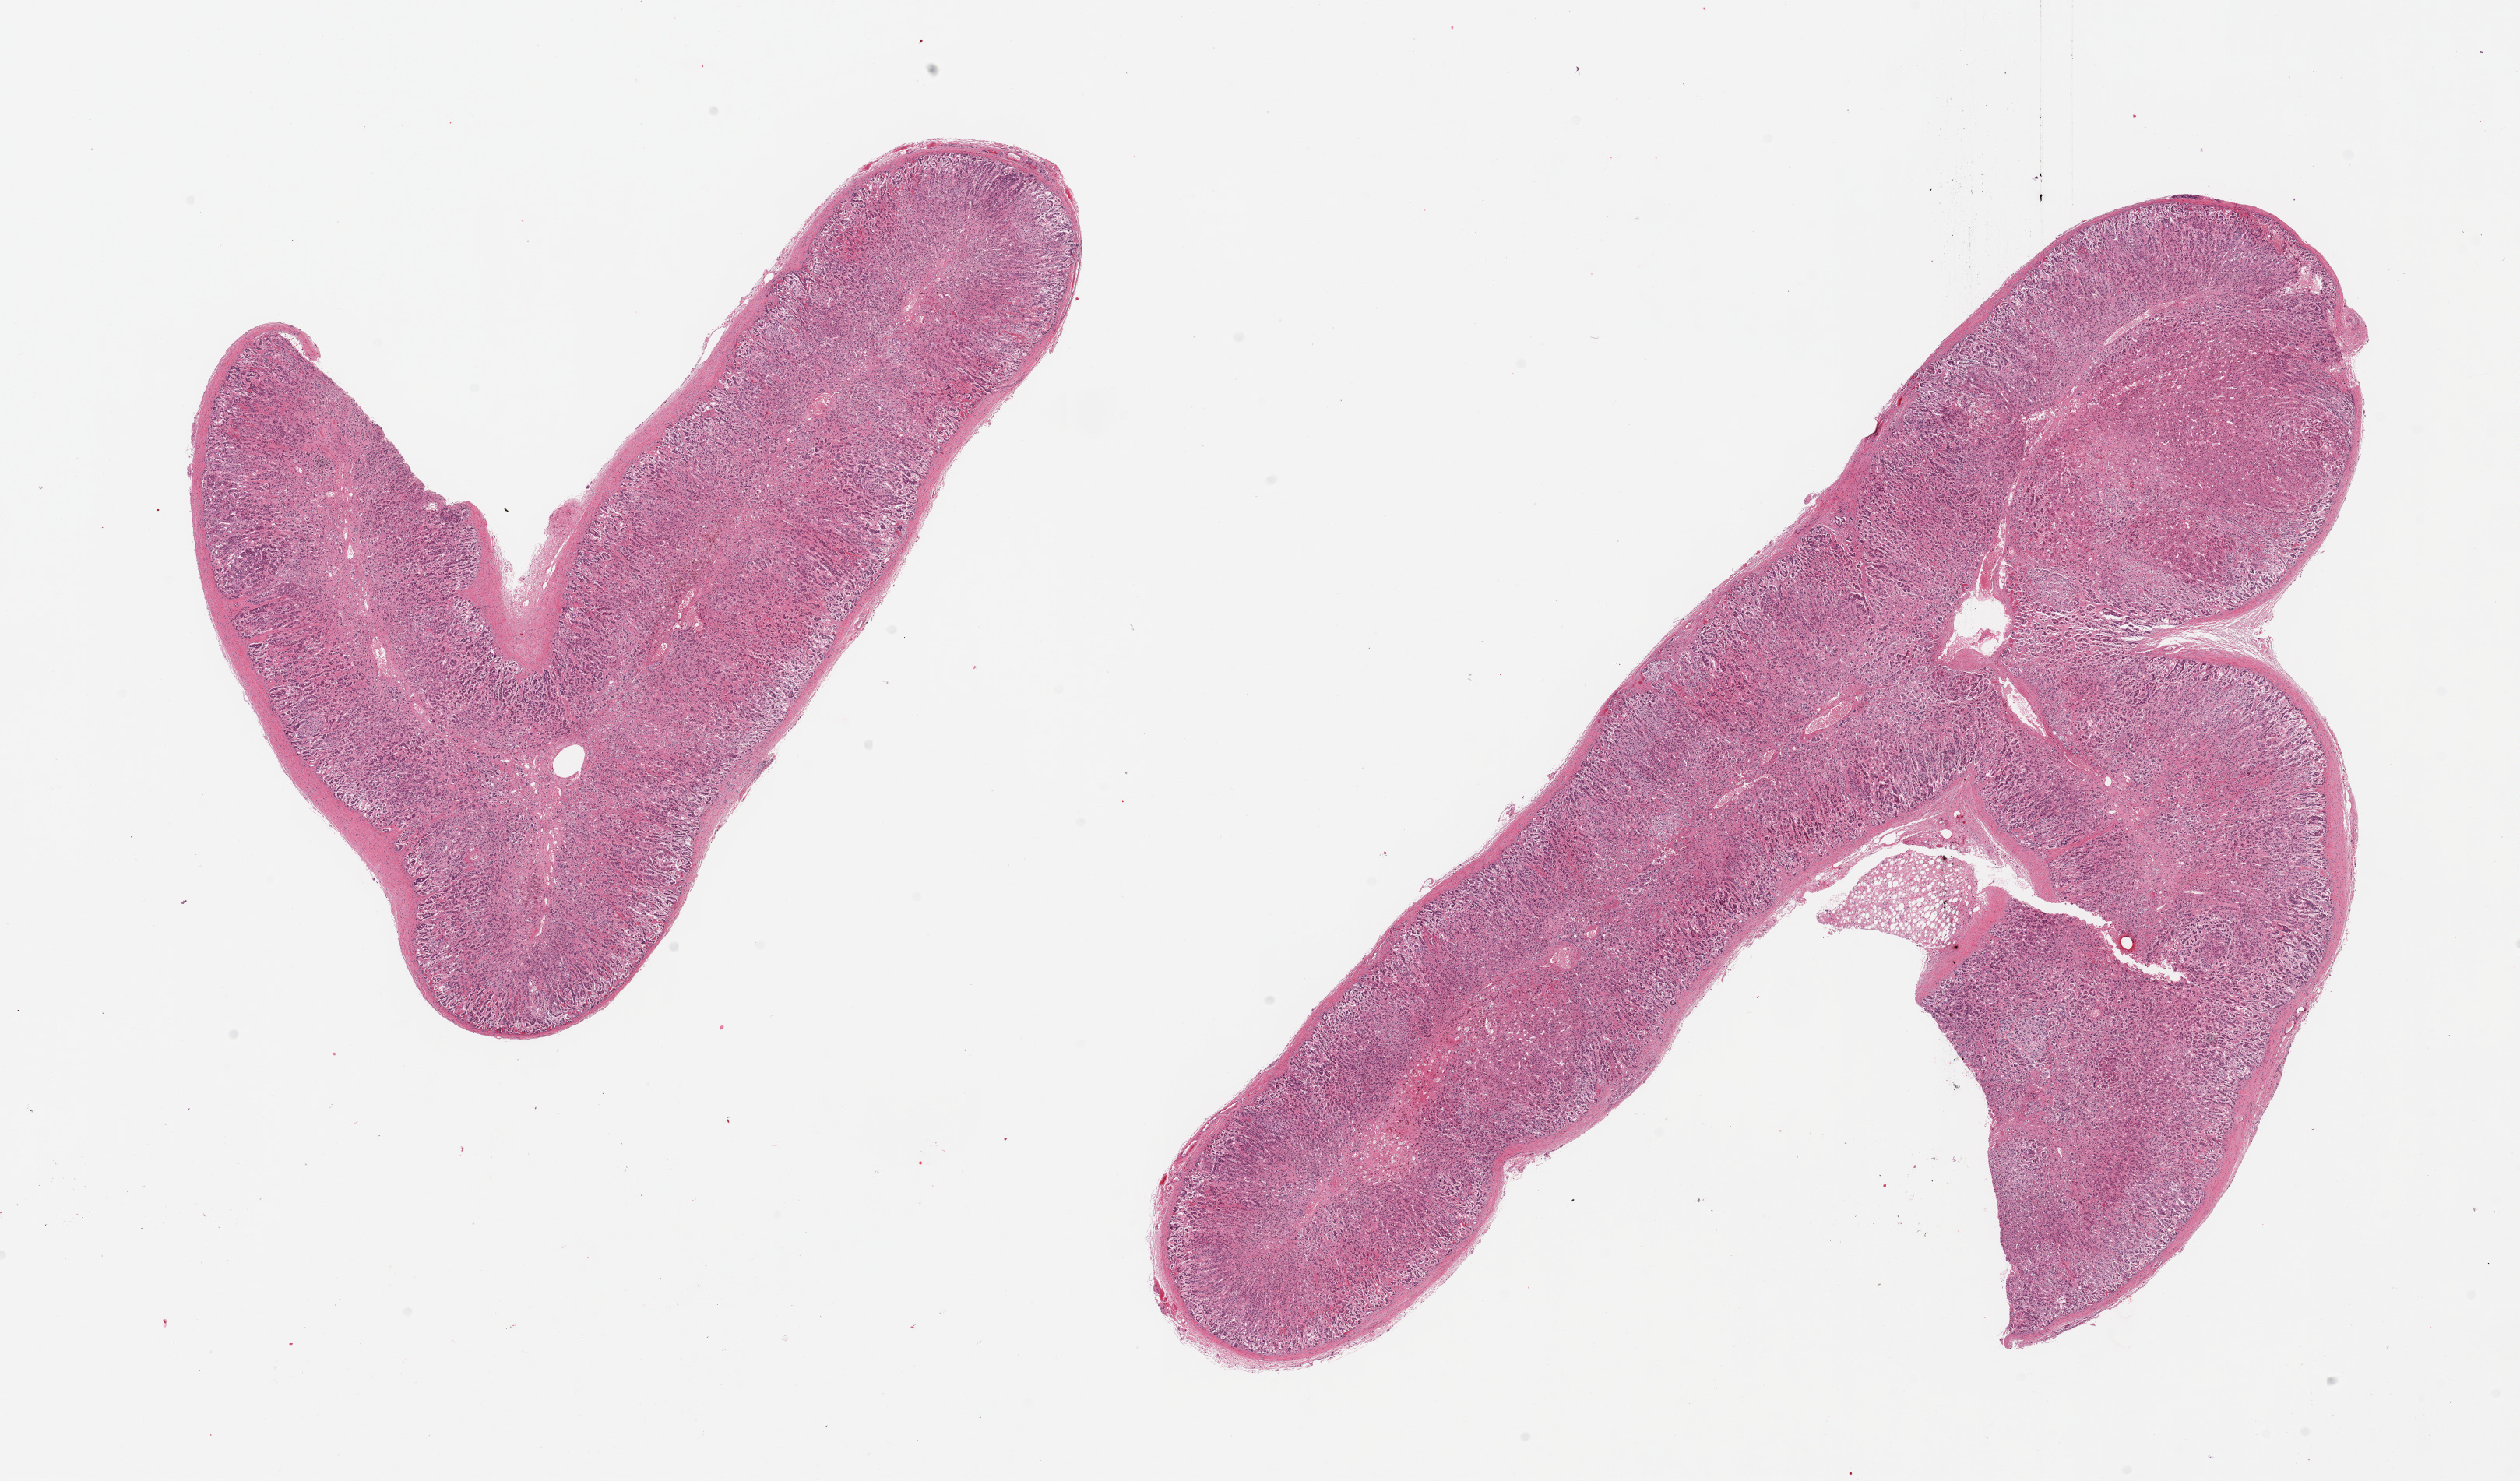
Digitized hematoxylin and eosin (H&E)-stained section — a low-resolution overview of the entire scanned area, about 25.6 x 15.0 mm (slide scanned at 20x); PAXgene-fixed paraffin-embedded (PFPE) section; target tissue: adrenal gland; tissue donor sample. Donor: female.
Reviewer comment on this tissue sample: 2 pieces, all cortex, well preserved, minimal fat.